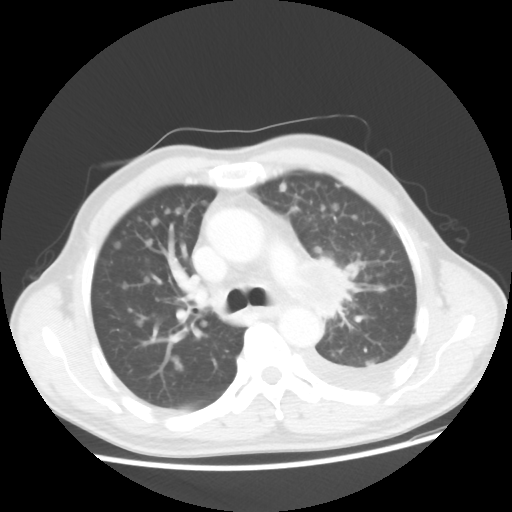
Chest CT, one axial slice; position 31 of 48 along the scan axis; reconstruction kernel STANDARD; 100 kVp; lung window (W 1500 / L -600 HU); 5 mm slice thickness; 512 × 512 image matrix, field of view 362 × 362 mm. Patient: male, 55 years. From the clinical record (not read from this slice): clinical TNM (as recorded): T2 N3 M1a; histopathological grade: G3.
Structures marked on this image (bounding box drawn by a radiologist):
- lung tumour (recorded histology: squamous cell carcinoma): bounding box (x1, y1, x2, y2) in pixels: (294, 248, 349, 319)